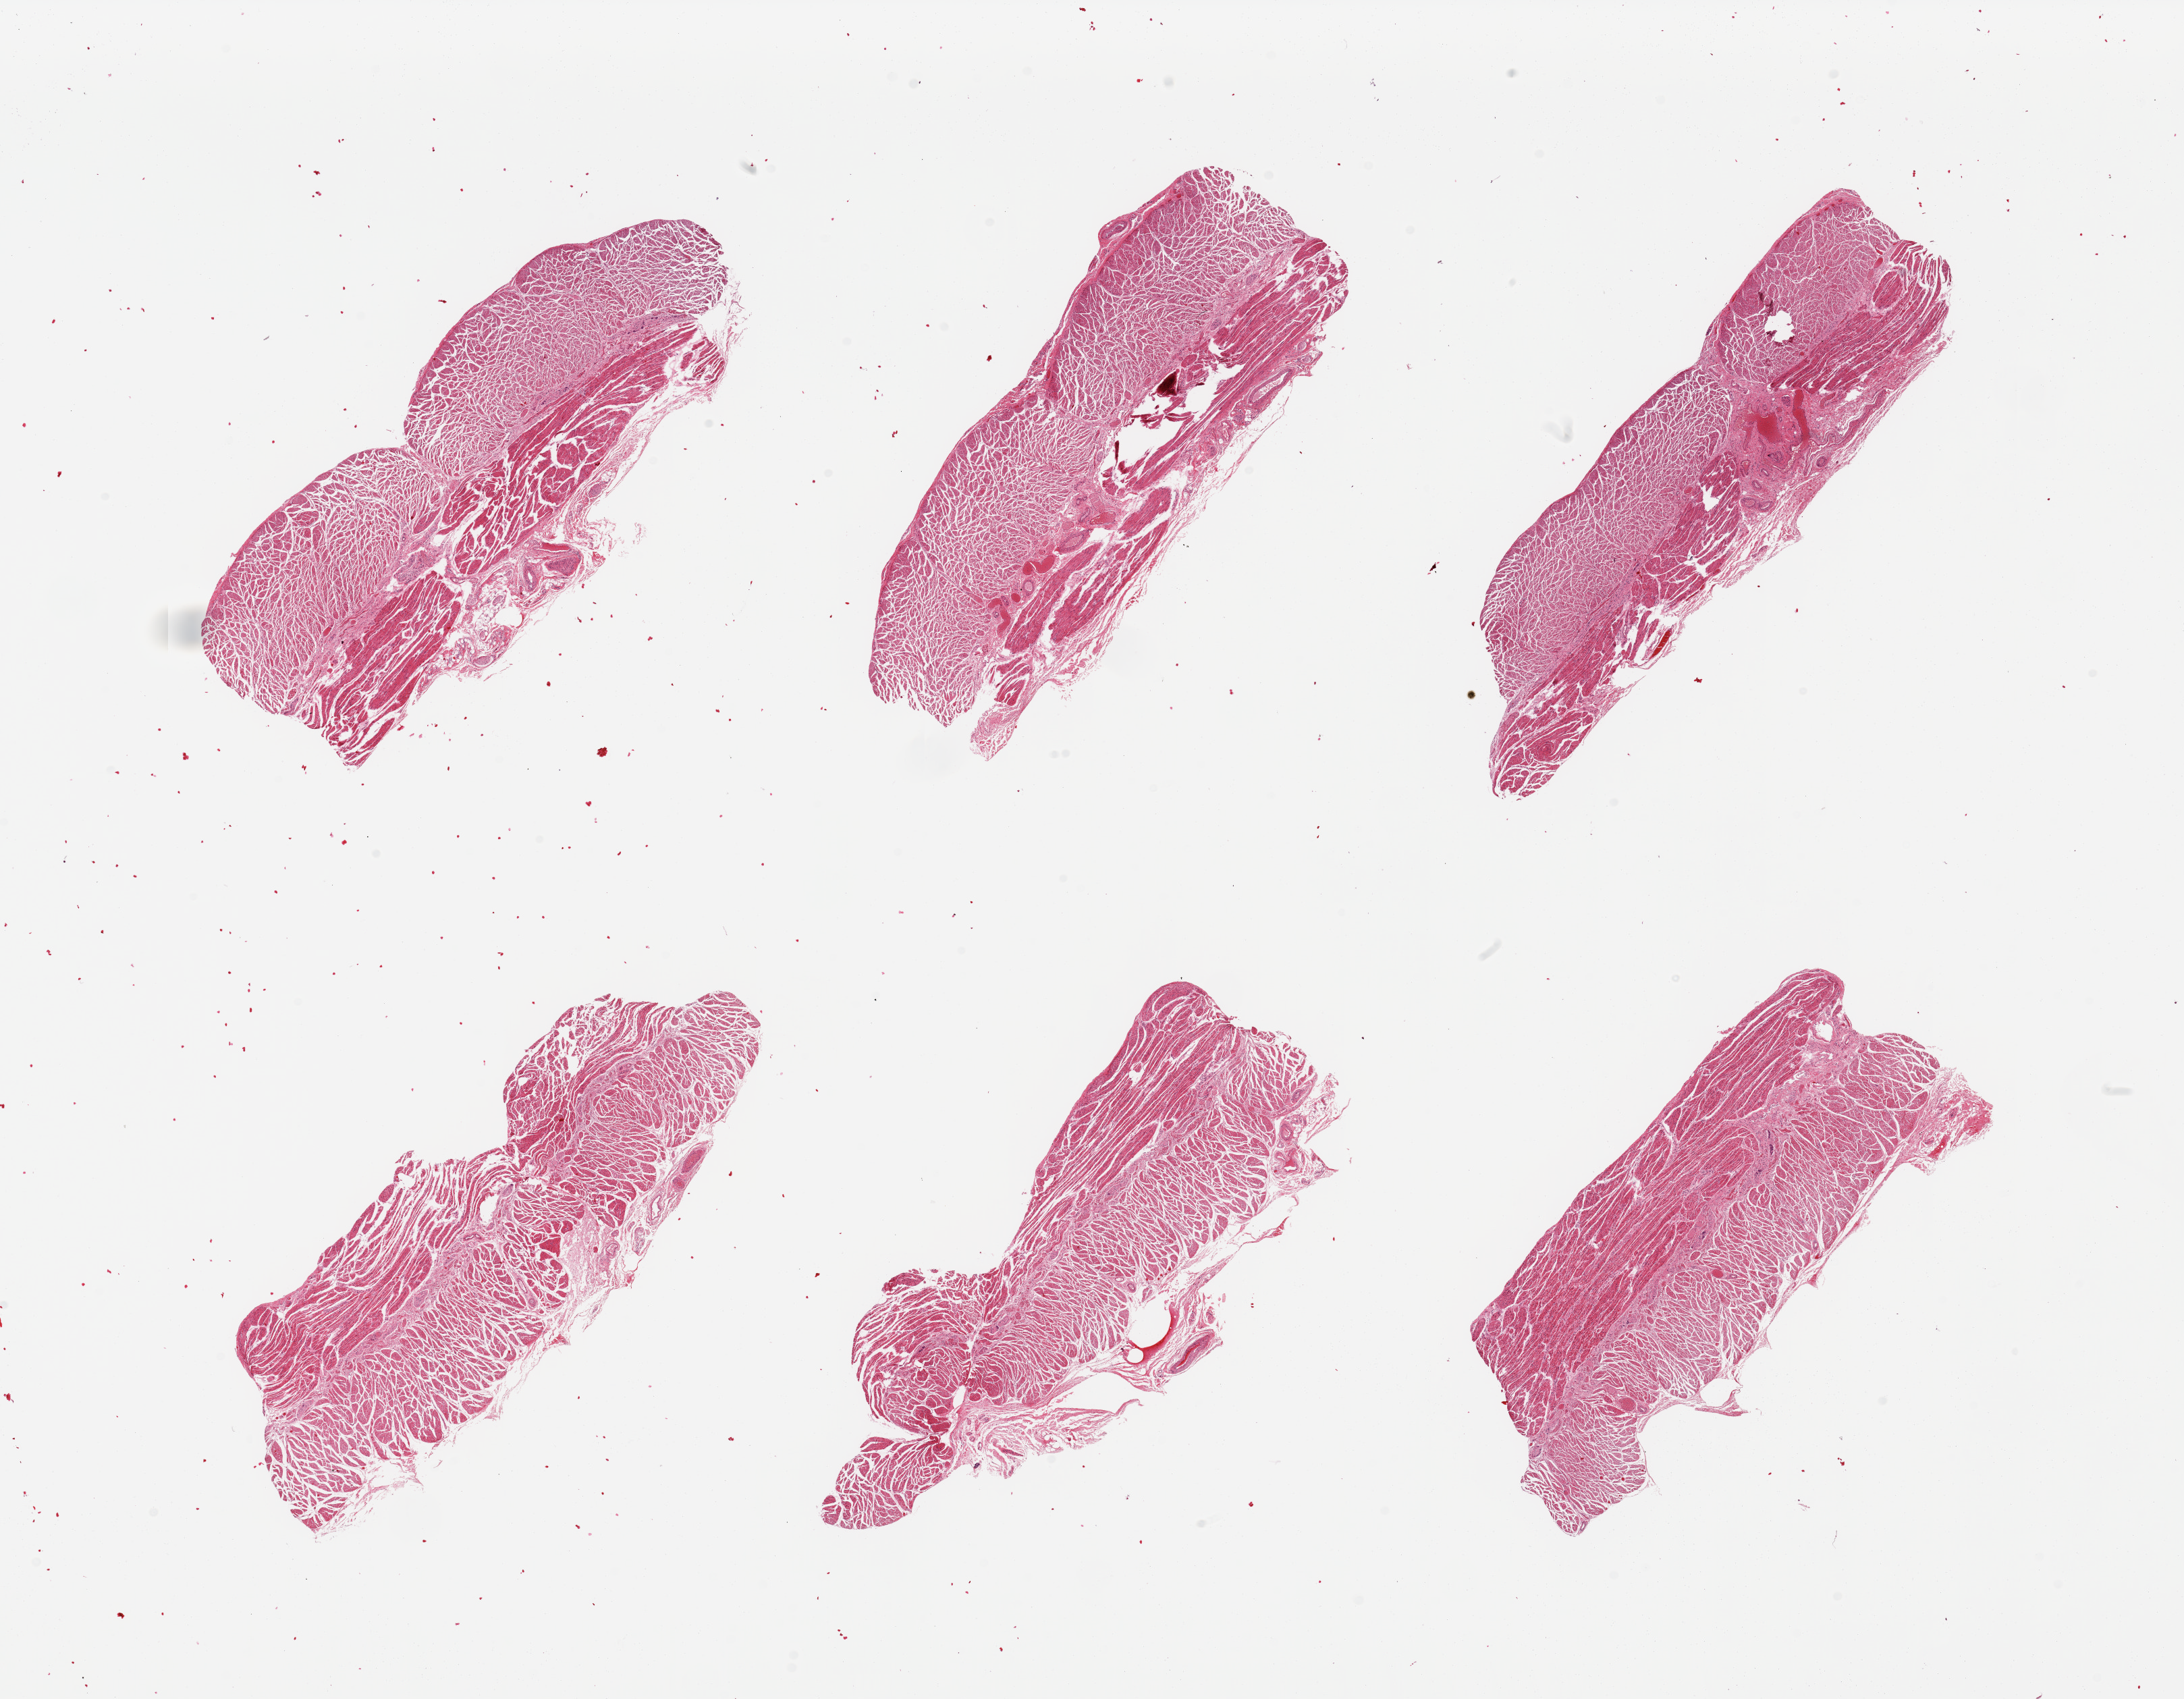
Digitized H&E-stained section — a low-resolution overview of the entire scanned area, about 25.6 x 19.9 mm (slide scanned at 20x); PAXgene-fixed paraffin-embedded (PFPE) section; sampled site (target tissue): esophageal muscle; tissue donor sample. Male donor.
- pathologist's review note for this sample: 6 pieces, muscularis, good speicmens